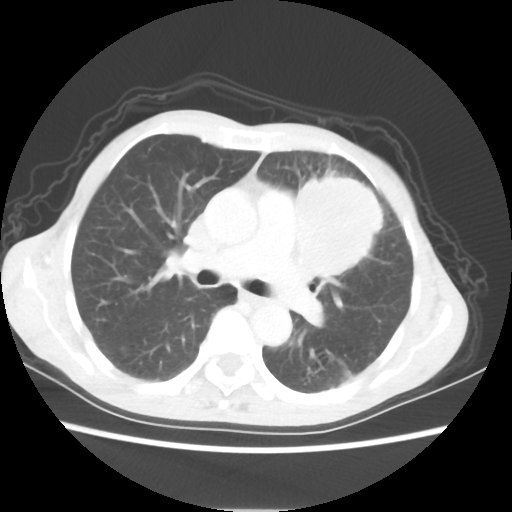
Chest CT, one axial slice; slice 36 of 56 in the series (ordered by position); reconstruction kernel STANDARD; lung window (W 1500 / L -600 HU); 5 mm slice thickness; 512 × 512 image matrix, field of view 331 × 331 mm. Patient: female, 60 years. From the clinical record (not read from this slice): clinical TNM (as recorded): T4 N1 M0.
Outlined on this slice (rectangle marked by the reading radiologist):
- lung tumour (recorded histology: adenocarcinoma): bounding box (x1, y1, x2, y2) in pixels: (287, 168, 384, 281)